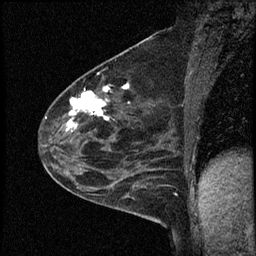
Breast MRI (dynamic contrast-enhanced), one sagittal slice. Dynamic contrast-enhanced study with each time point stored as its own series, time point 2 of 4 at this slice position (early post-contrast, ordered by acquisition time). 1.5 T. TE 4.2 ms, TR 17.6 ms. 256 × 256 image matrix, field of view 200 × 200 mm. Female patient, age 53 years. Case-level facts recorded for this patient, not image findings: setting: breast cancer imaged before/during neoadjuvant chemotherapy; receptor status: HR-positive, HER2-negative.
Structures marked on this image (semi-automatically segmented with operator editing):
- analysis volume of interest (the breast-tissue region the enhancement analysis was run in; not a lesion): bounding box <42,69,156,199> (left, top, right, bottom; pixels)
- tumour enhancement mask (voxels above the 100 % enhancement threshold inside the analysis volume of interest): <67,85,129,131>